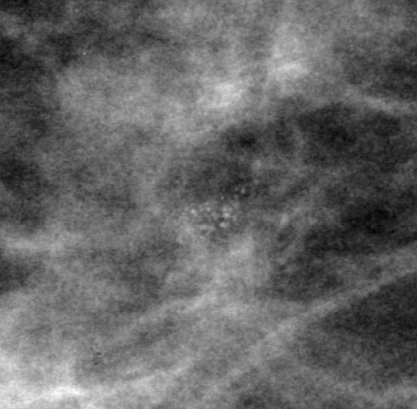
Crop from a digitized film mammogram around one marked abnormality; left breast; CC view; BI-RADS breast density category 3 (scale 1–4).
- Finding: calcifications, morphology pleomorphic, distribution clustered; BI-RADS assessment category 4; pathology result (as recorded, not read from the image): malignant.